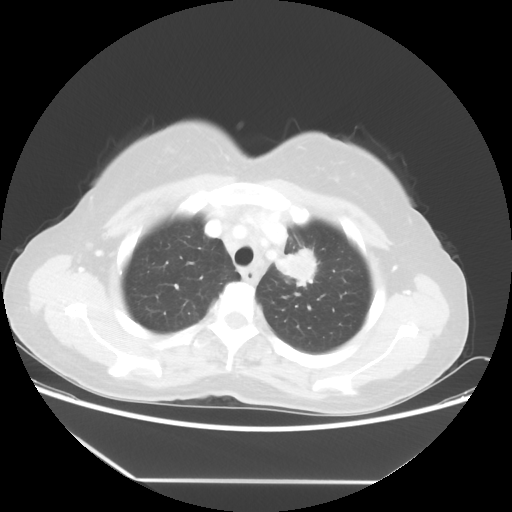
Chest CT, one axial slice. Position 43 of 52 along the scan axis. Reconstruction kernel STANDARD. 100 kVp. Lung window (W 1500 / L -600 HU). 5 mm slice thickness. 512 × 512 image matrix, field of view 390 × 390 mm. Patient: female, 50 years. Case-level facts recorded for this patient, not image findings: clinical TNM (as recorded): T2 N3 M0.
Outlined on this slice (rectangle marked by the reading radiologist):
- lung tumour (recorded histology: adenocarcinoma): box from (x=270, y=240) to (x=318, y=285) px